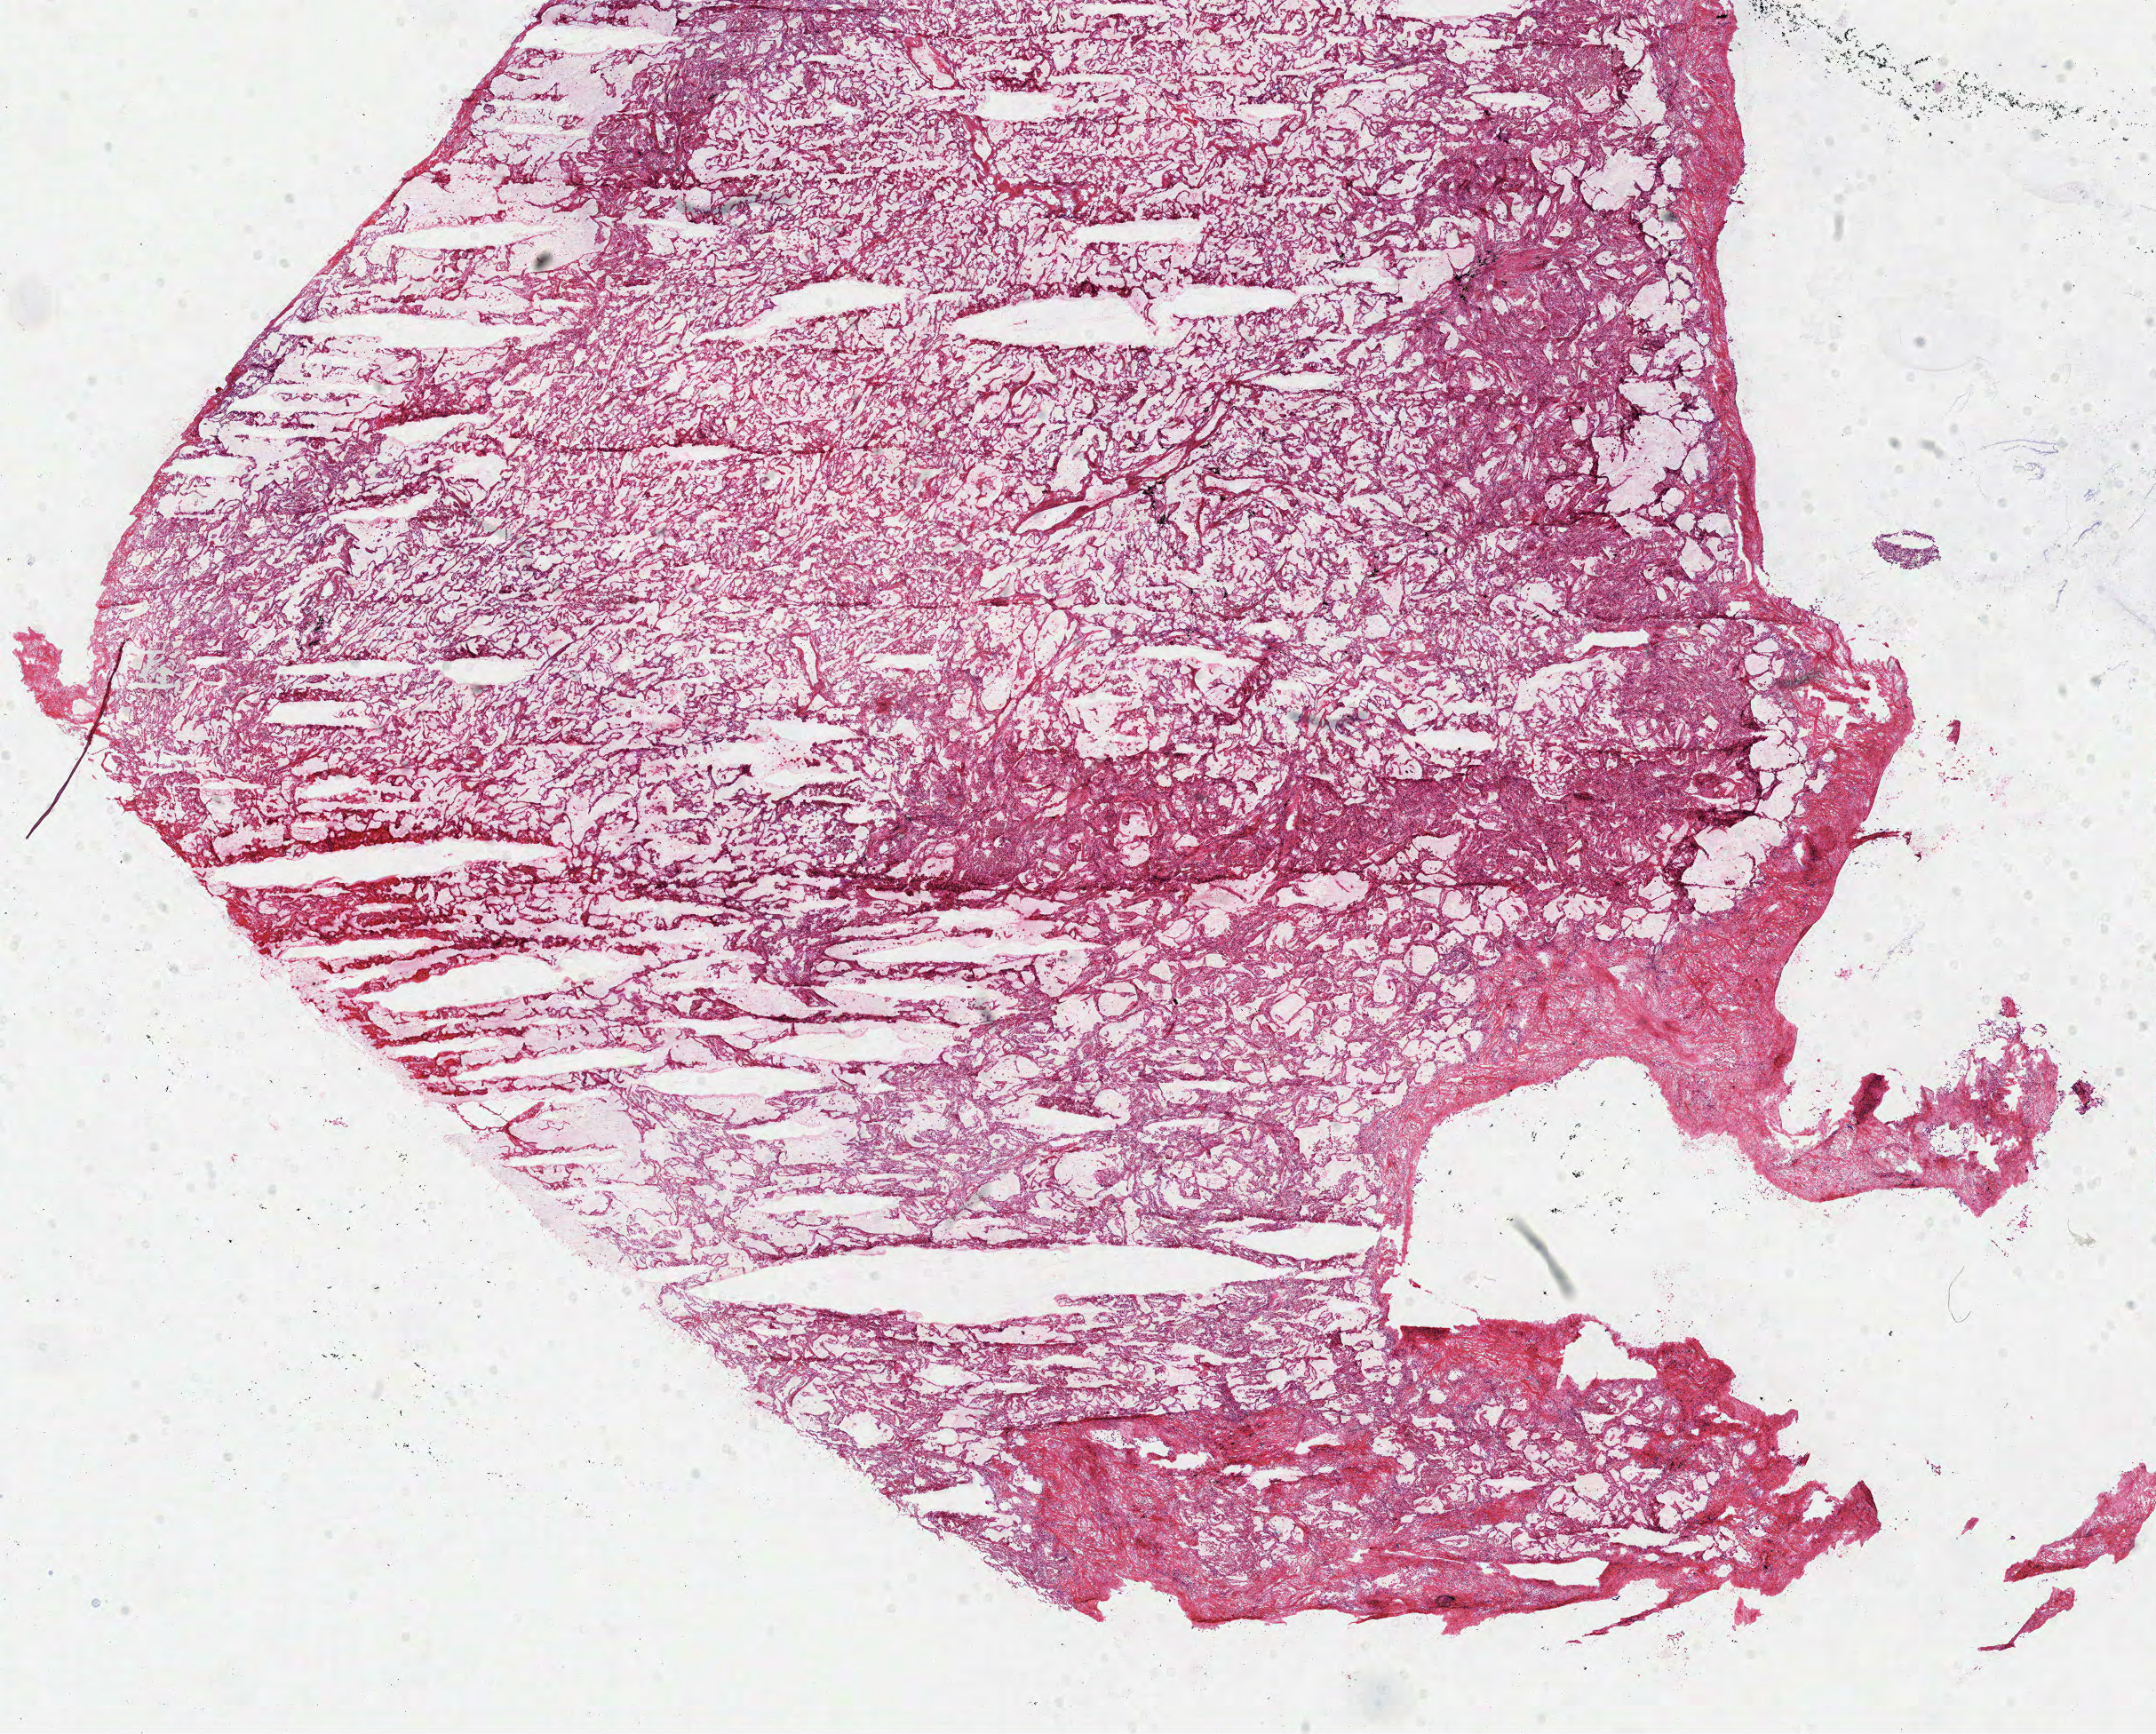
Digitized H&E-stained tissue section (whole slide), shown as a low-resolution overview of the whole scanned area (about 19.1 x 15.4 mm); frozen section from the top of the tissue portion; solid tissue normal (non-tumour tissue) sample from the lung. Patient: male, age at initial diagnosis 58 years.
This section: solid tissue normal sample (biorepository sample class). Patient diagnosis: Mucinous adenocarcinoma (lower lobe, lung).